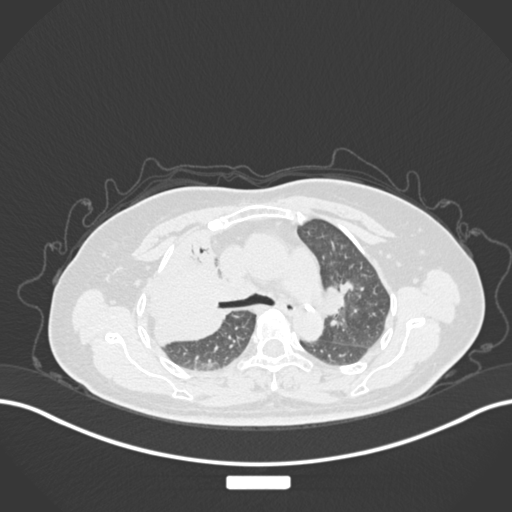
Chest CT, one axial slice. Position 104 of 177 along the scan axis. Lung window (W 1500 / L -600 HU). 1 mm slice thickness. 512 × 512 image matrix, field of view 400 × 400 mm. Patient: female, 60 years. Case-level facts recorded for this patient, not image findings: clinical TNM (as recorded): T3 N1 M1.
Structures marked on this image (rectangle marked by the reading radiologist):
- lung tumour (recorded histology: adenocarcinoma): bounding box (x1, y1, x2, y2) in pixels: (141, 244, 229, 348)